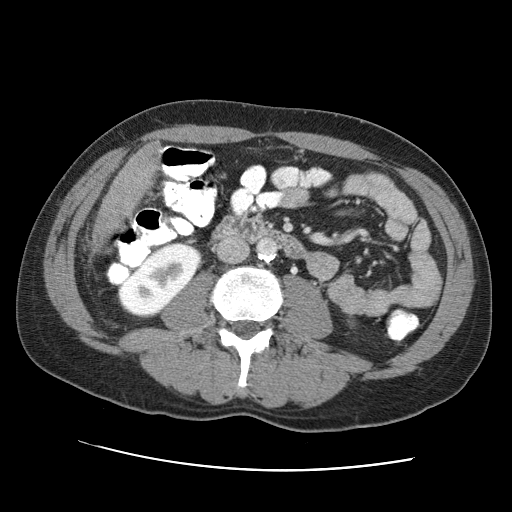
Contrast-enhanced abdominal CT (liver protocol), one axial slice. Position 8 of 95 along the scan axis. 120 kVp. One of 2 acquisitions stored at this slice position. Soft-tissue window (W 400 / L 40 HU). 512 × 512 image matrix, field of view 360 × 360 mm. From the clinical record (not read from this slice): diagnosis: hepatocellular carcinoma (patient treated with transarterial chemoembolisation; whether this scan precedes or follows treatment is not stated here); TNM stage (as recorded): Stage-IVA; Child-Pugh class: A.
Annotated regions visible in this slice (semi-automatically segmented with operator editing):
- liver parenchyma outside the tumour (the mass and vessels are separate outlines, so this box may not span the whole liver): bounding box [x1, y1, x2, y2] px = [92, 146, 156, 248]